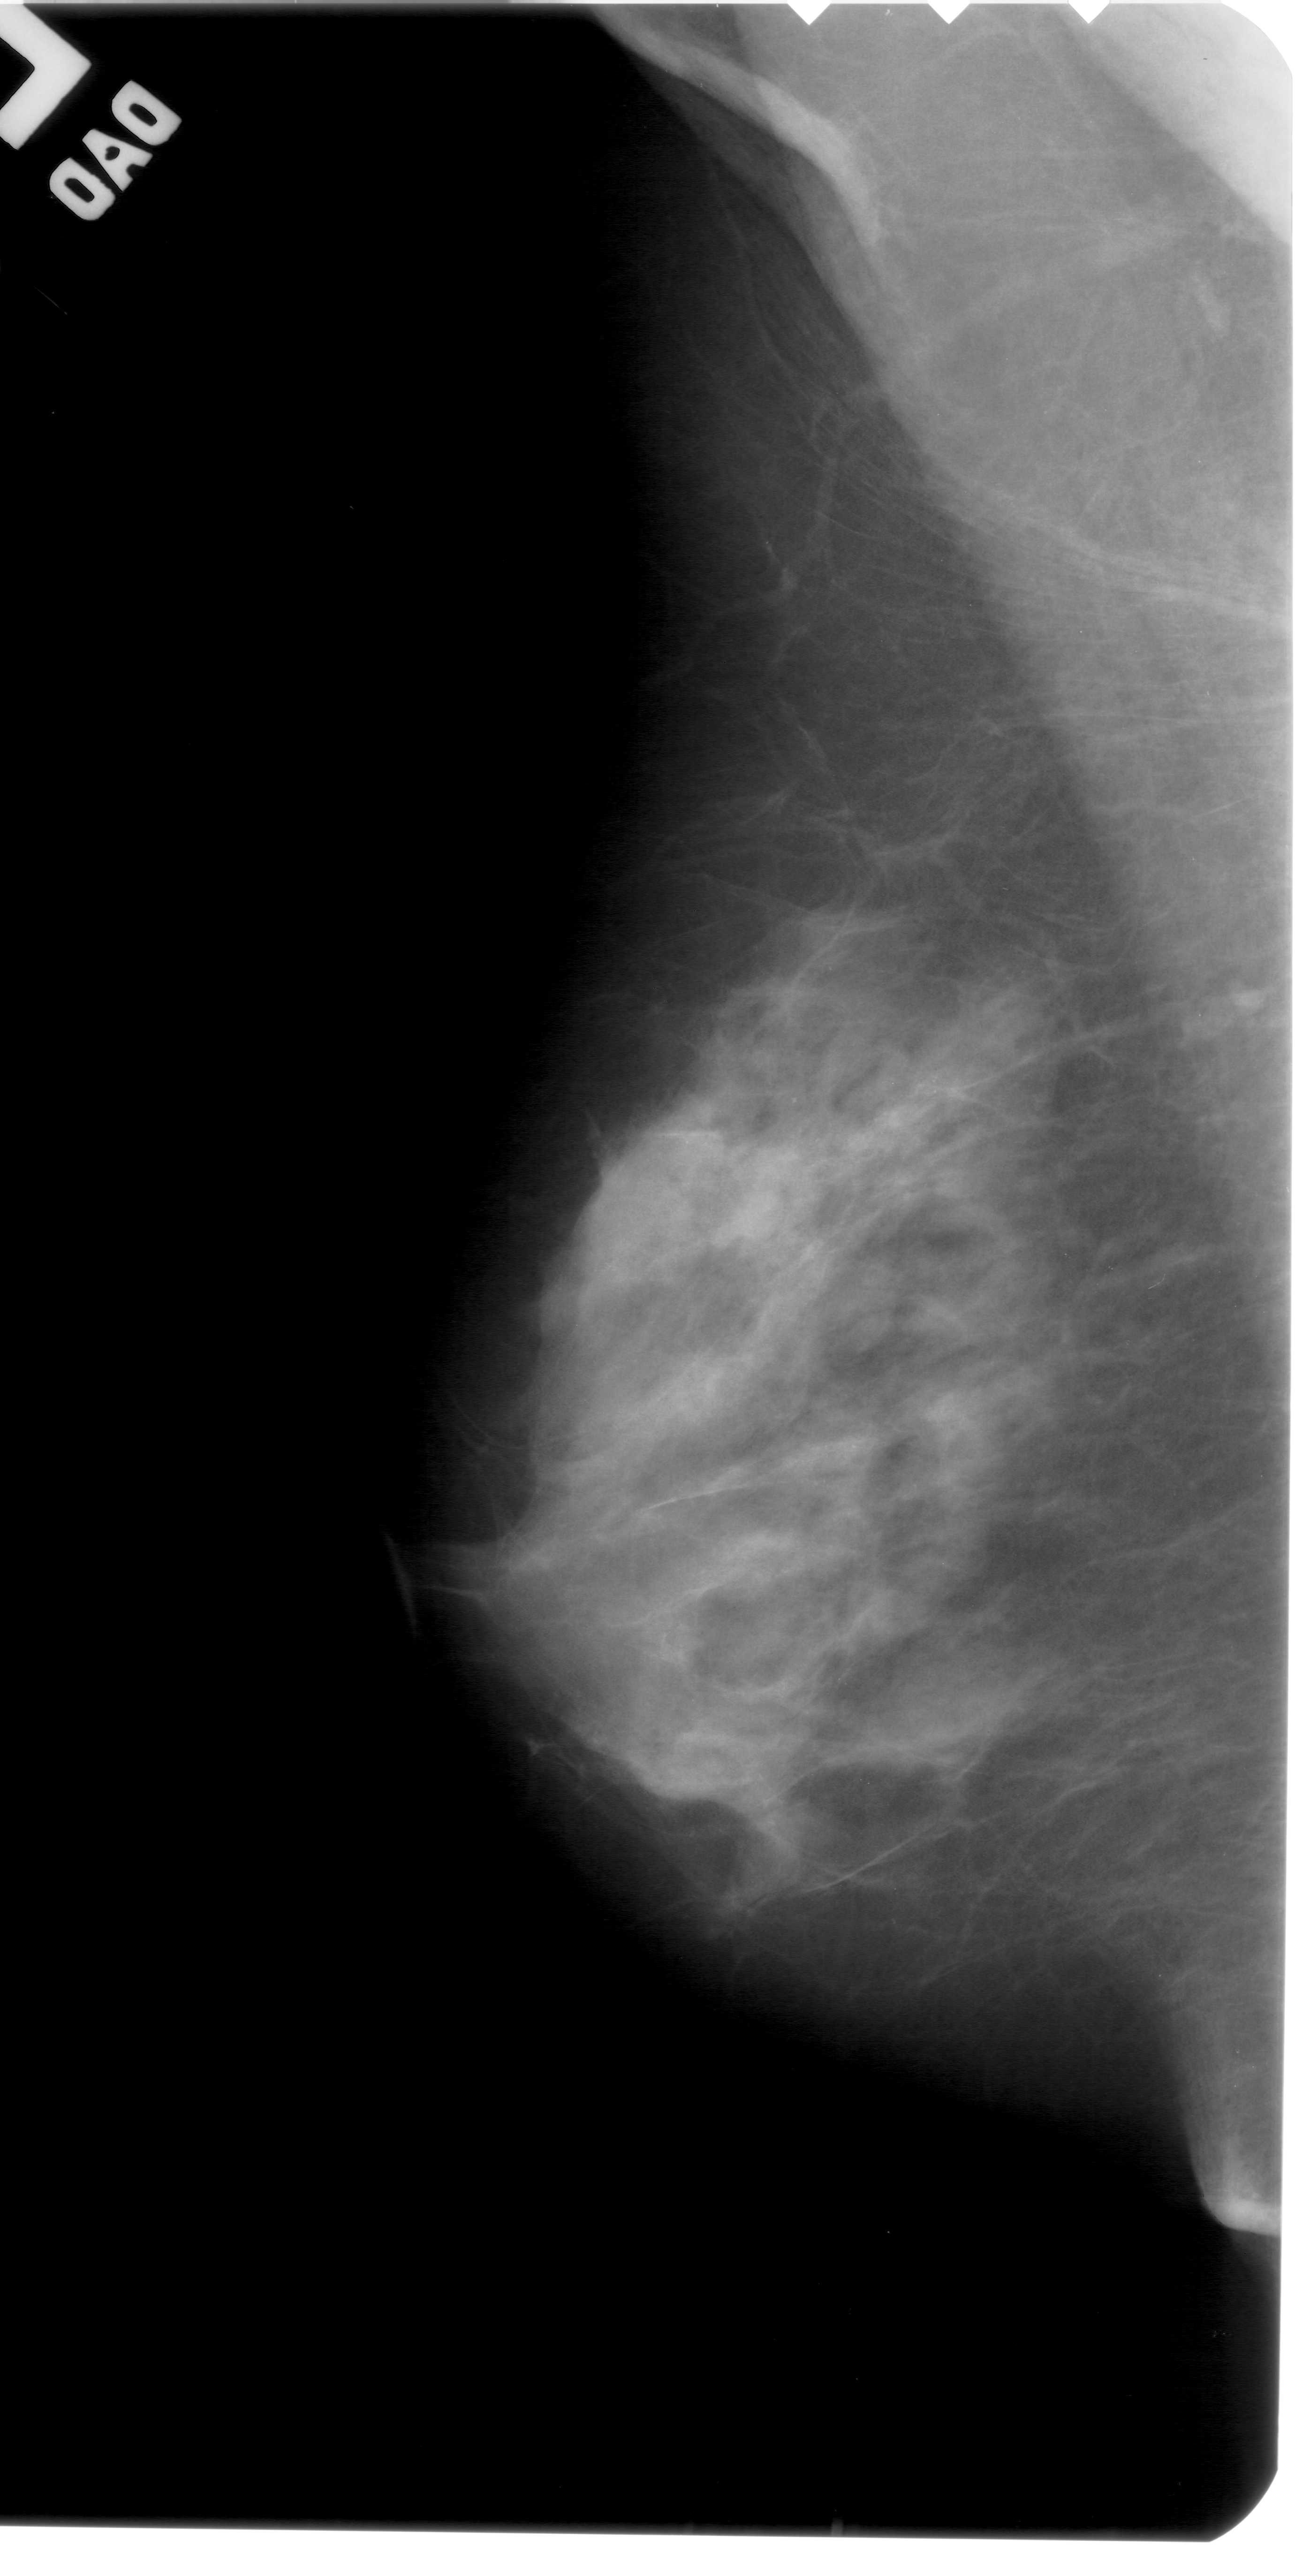
Digitized screen-film mammogram; left breast; mediolateral oblique (MLO) view; breast composition: extremely dense (BI-RADS density category 4 of 4); 1302 × 2576 image matrix.
Expert-marked regions of interest on this film, with their recorded descriptors:
- calcifications, morphology punctate, distribution linear; BI-RADS assessment category 4; subtlety rating 1 on a 1 (subtle) to 5 (obvious) scale; pathology (as recorded): benign: bounding box [x1, y1, x2, y2] px = [775, 1048, 976, 1148]